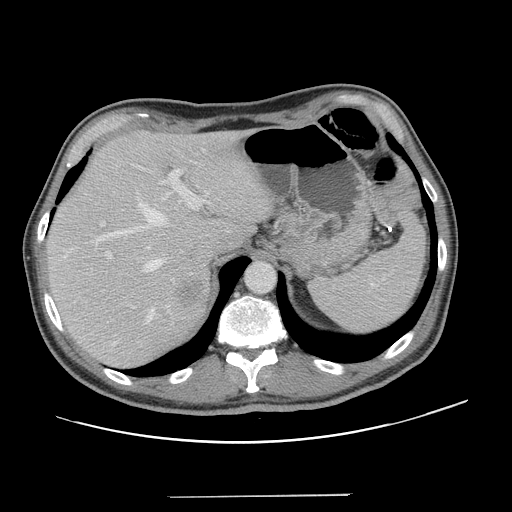
Contrast-enhanced abdominal CT, one axial slice. Slice 98 of 131 in the series (ordered by position). Intravenous contrast given. Soft-tissue window (W 400 / L 40 HU). 512 × 512 image matrix, field of view 403 × 403 mm. Male patient, age 60 years. From the clinical record (not read from this slice): diagnosis: colorectal cancer liver metastases, imaged before liver resection; multiple liver metastases: no; largest metastasis: 2.5 cm.
Annotated regions visible in this slice (manually delineated by an expert):
- hepatic veins: bounding box [x1, y1, x2, y2] px = [94, 192, 174, 323]
- liver: [47, 133, 269, 367]
- planned liver remnant (the part of the liver to remain after resection): [47, 133, 268, 353]
- portal vein (with intrahepatic branches): [99, 144, 211, 260]
- liver metastasis: [176, 277, 203, 308]